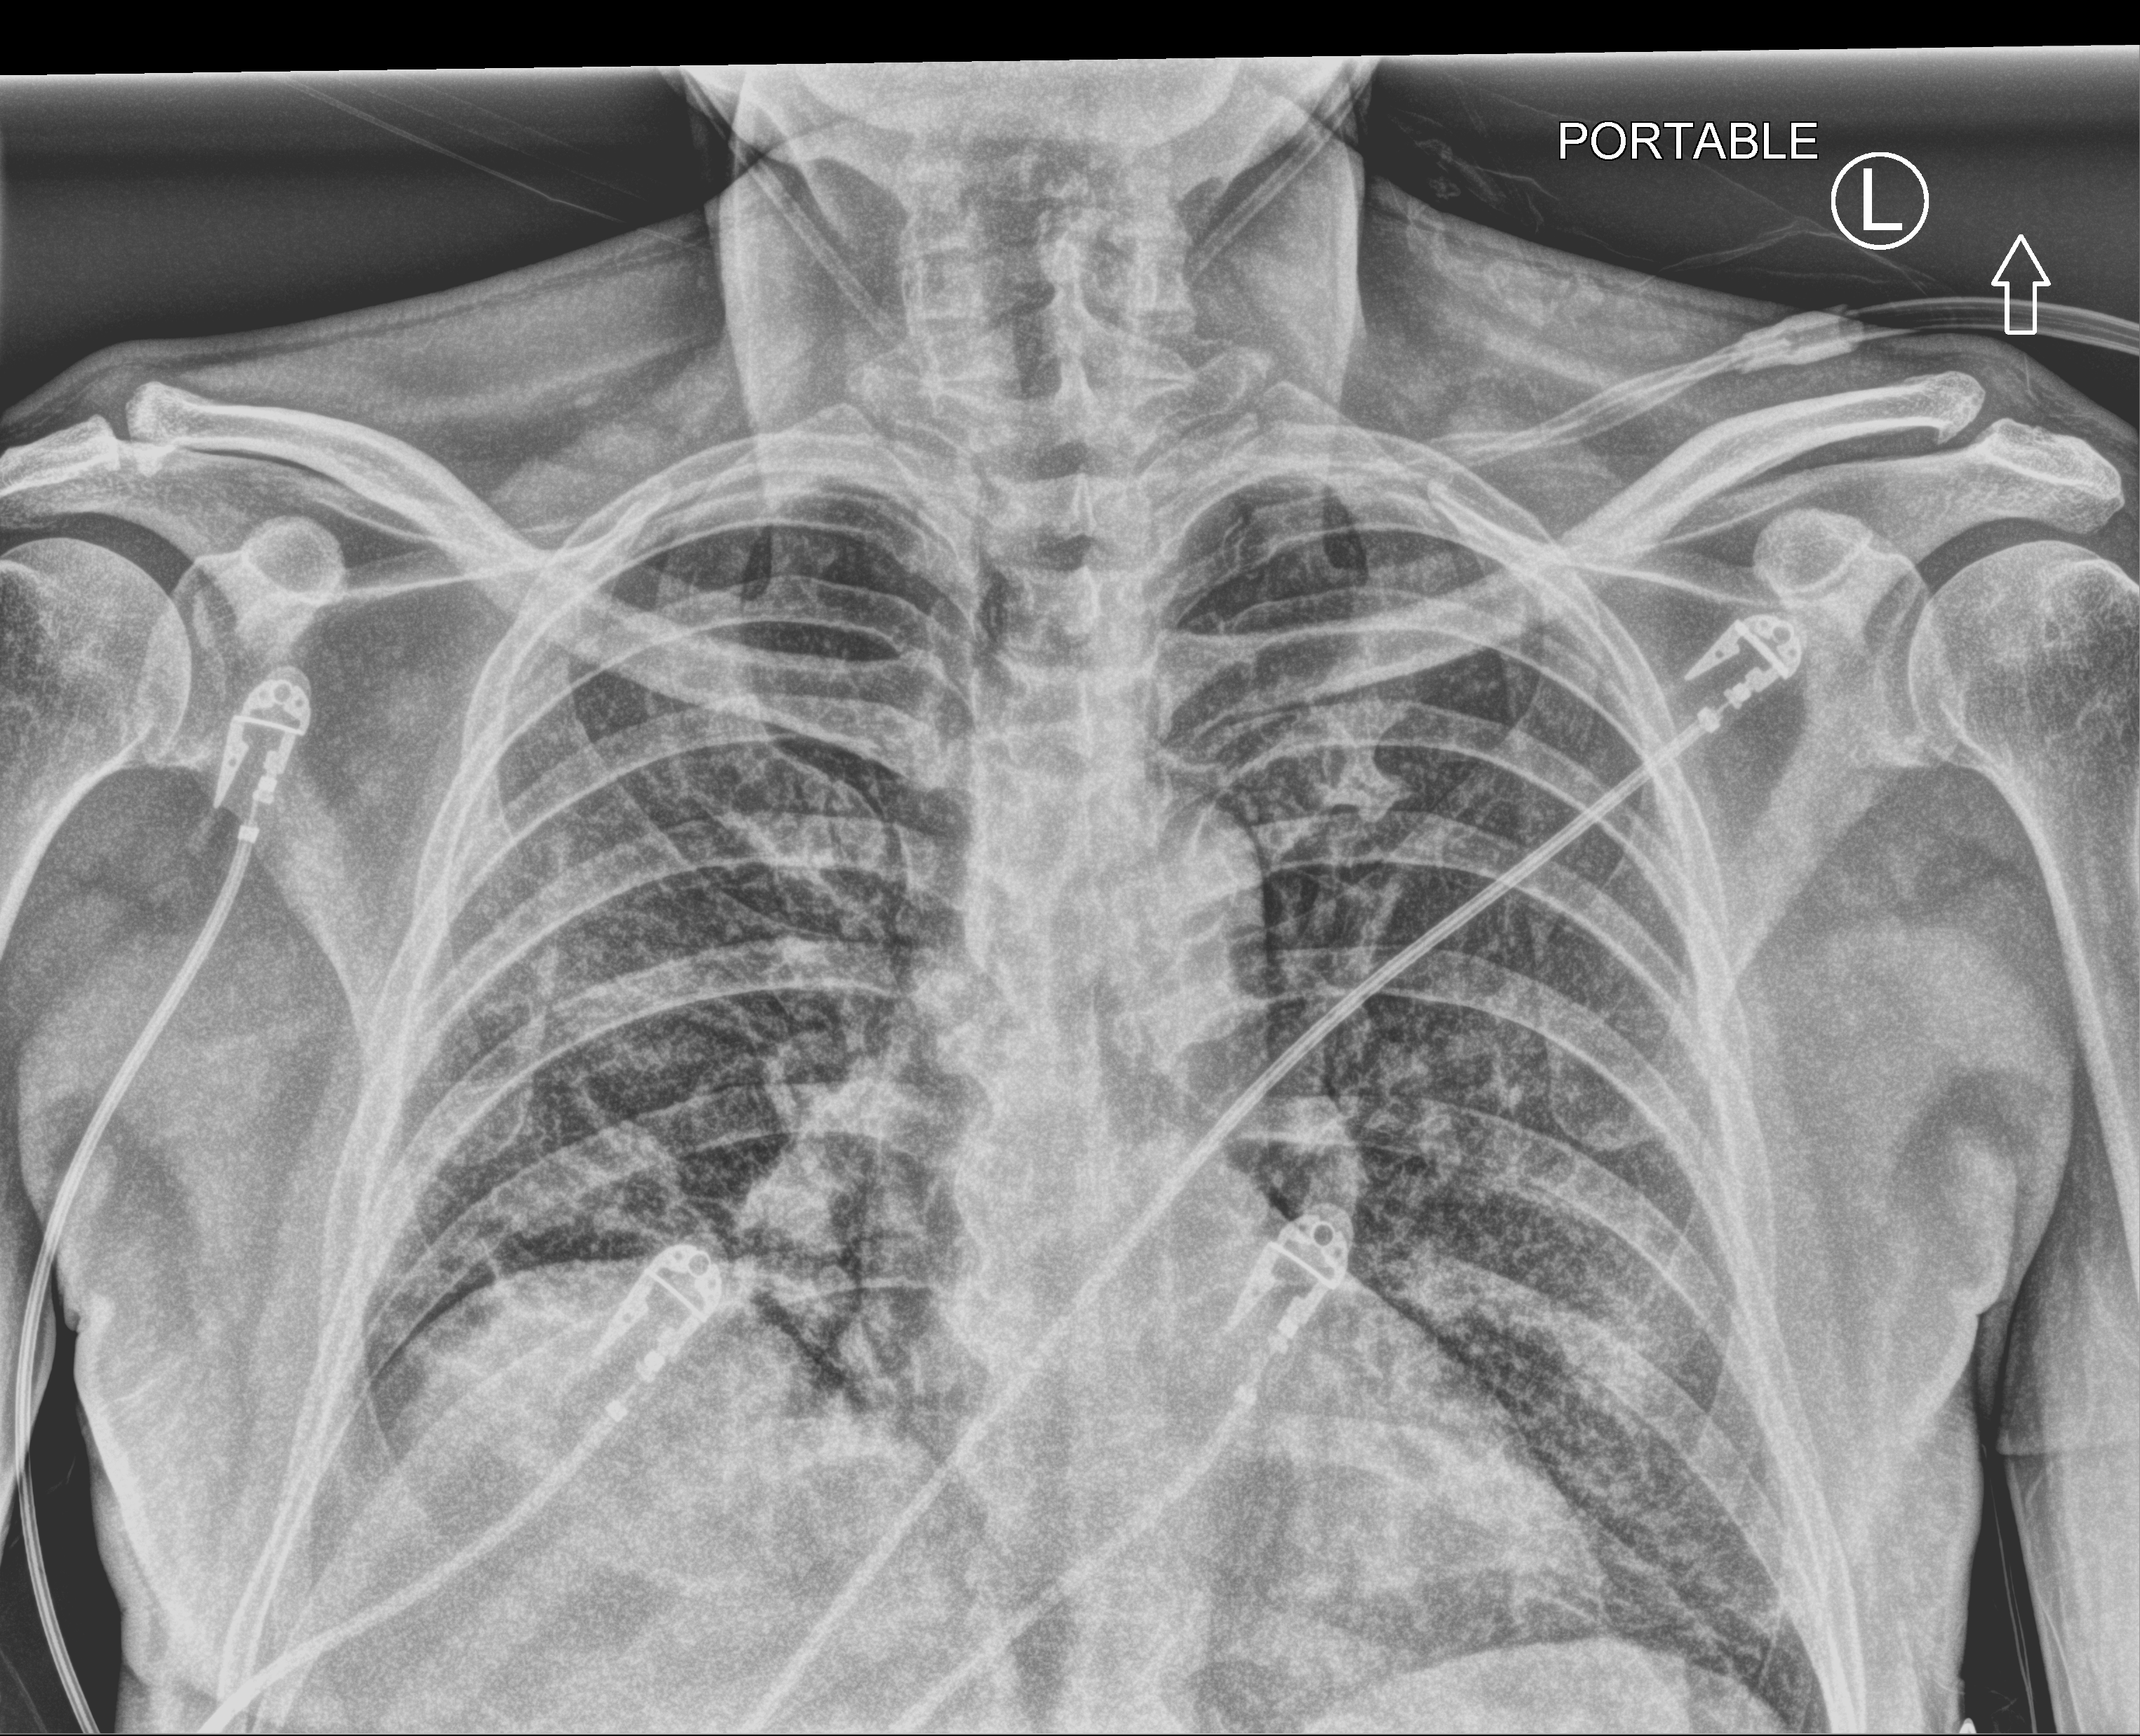
Chest X-ray (portable). Patient hospitalised with COVID-19; male, aged 60–74 years.
From the hospital-stay record, not from the radiograph (when in the stay this image was taken is not recorded): mechanically ventilated during this hospital stay: no.